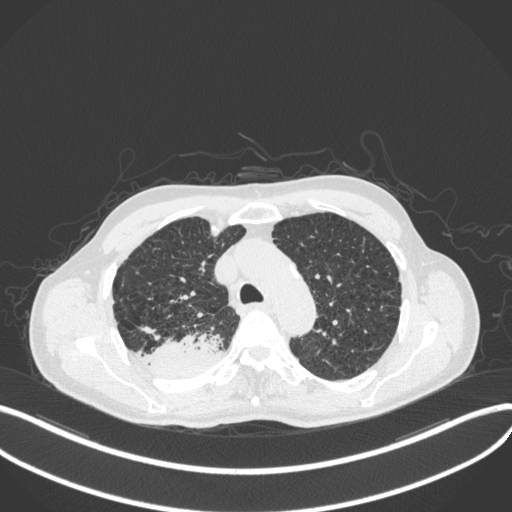
Chest CT, one axial slice. Position 330 of 423 along the scan axis. 120 kVp. Lung window (W 1500 / L -600 HU). 1 mm slice thickness. 512 × 512 image matrix, field of view 400 × 400 mm. Male patient, age 79 years. Case-level facts recorded for this patient, not image findings: clinical TNM (as recorded): T3 N0 M0.
Annotated regions visible in this slice (rectangle marked by the reading radiologist):
- lung tumour (recorded histology: adenocarcinoma): box from (x=147, y=333) to (x=222, y=379) px